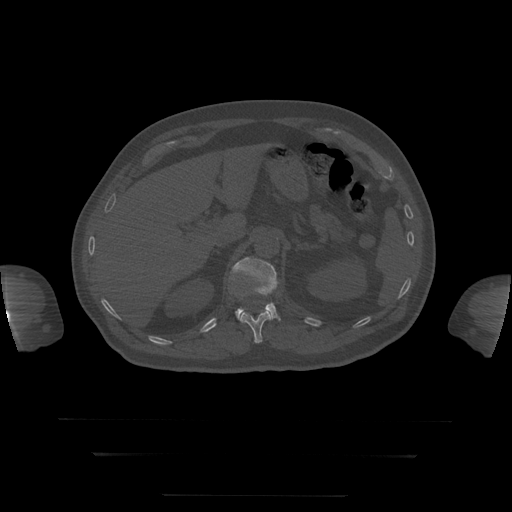
CT including the spine, one axial slice; slice 63 of 397 in the series (ordered by position); reconstruction kernel STANDARD; 120 kVp; bone window (W 1800 / L 400 HU); 1.25 mm slice thickness; 512 × 512 image matrix, field of view 510 × 510 mm. Patient age 73 years. From the clinical record (not read from this slice): primary cancer: prostate.
Outlined on this slice (semi-automatic segmentation, software-assisted and operator-edited):
- L1 vertebra: box from (x=231, y=257) to (x=280, y=320) px
- T12 vertebra: (x=240, y=295)–(x=271, y=344)
- T8 vertebra: (x=265, y=309)–(x=268, y=311)